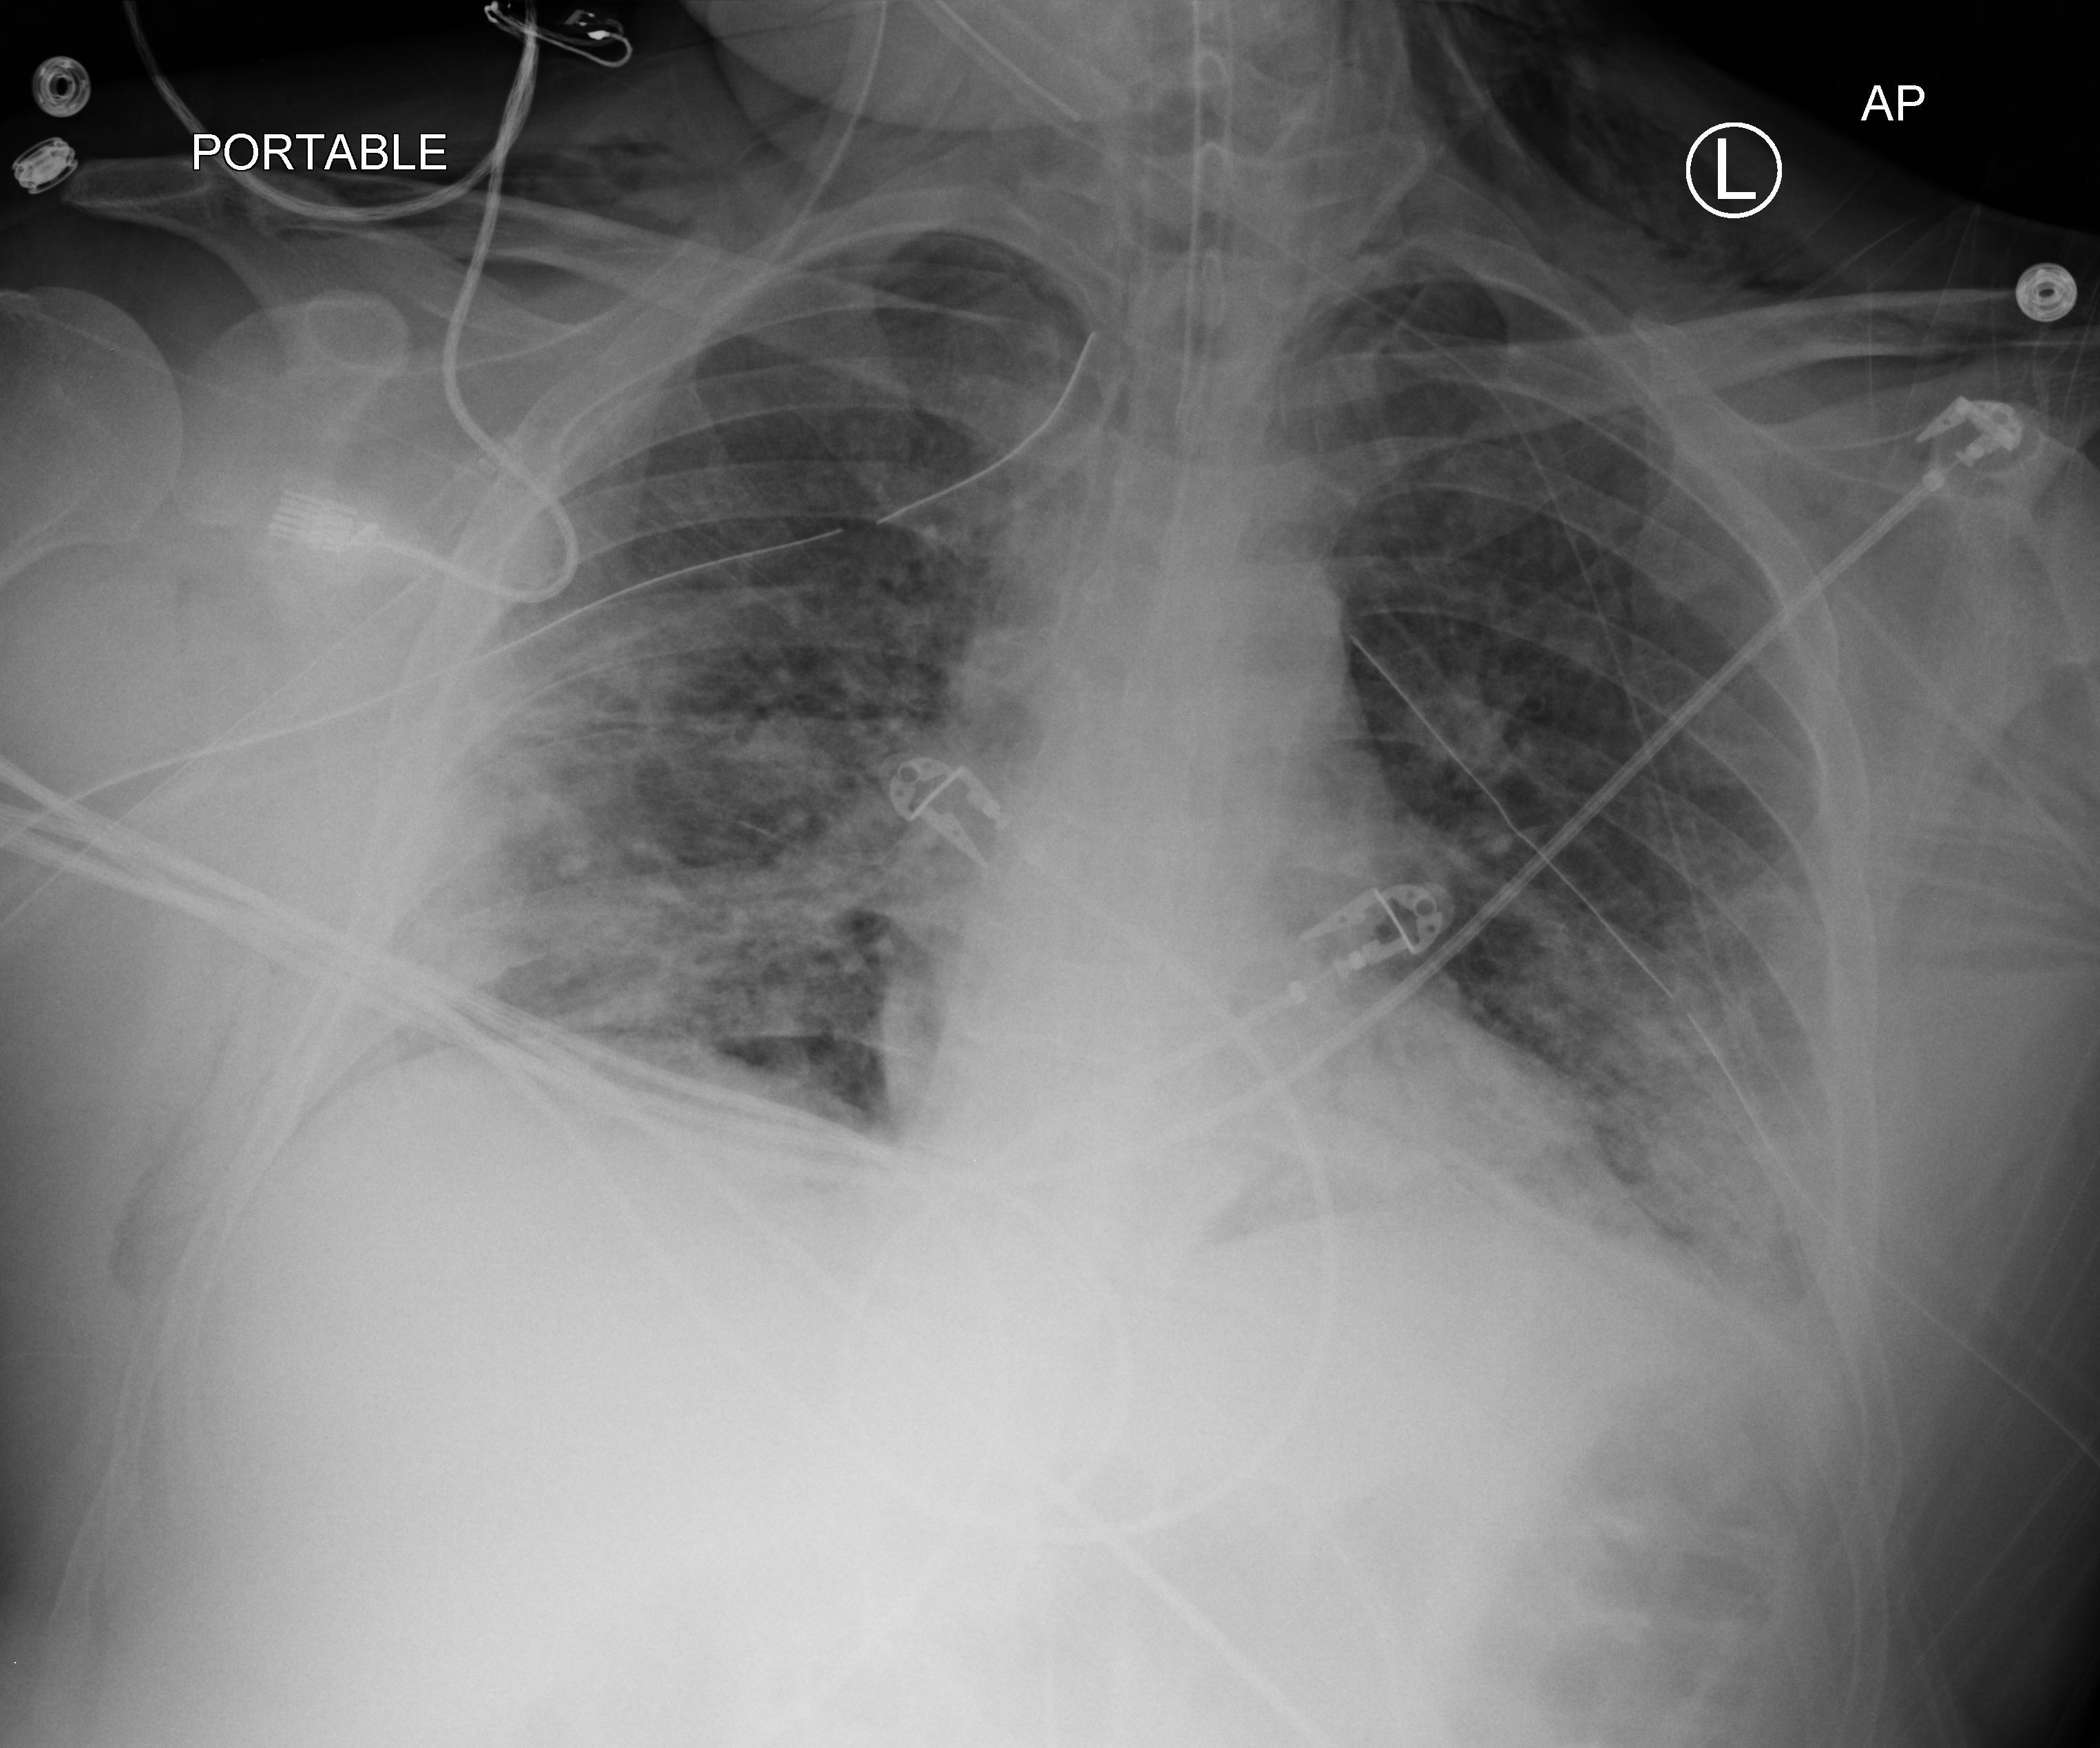
Chest X-ray (portable); anteroposterior (AP) projection. Patient hospitalised with COVID-19; male, aged 18–59 years.
From the hospital-stay record, not from the radiograph (when in the stay this image was taken is not recorded): COPD (admission record): no; smoking status (admission record): never; admitted to intensive care during this hospital stay: yes.